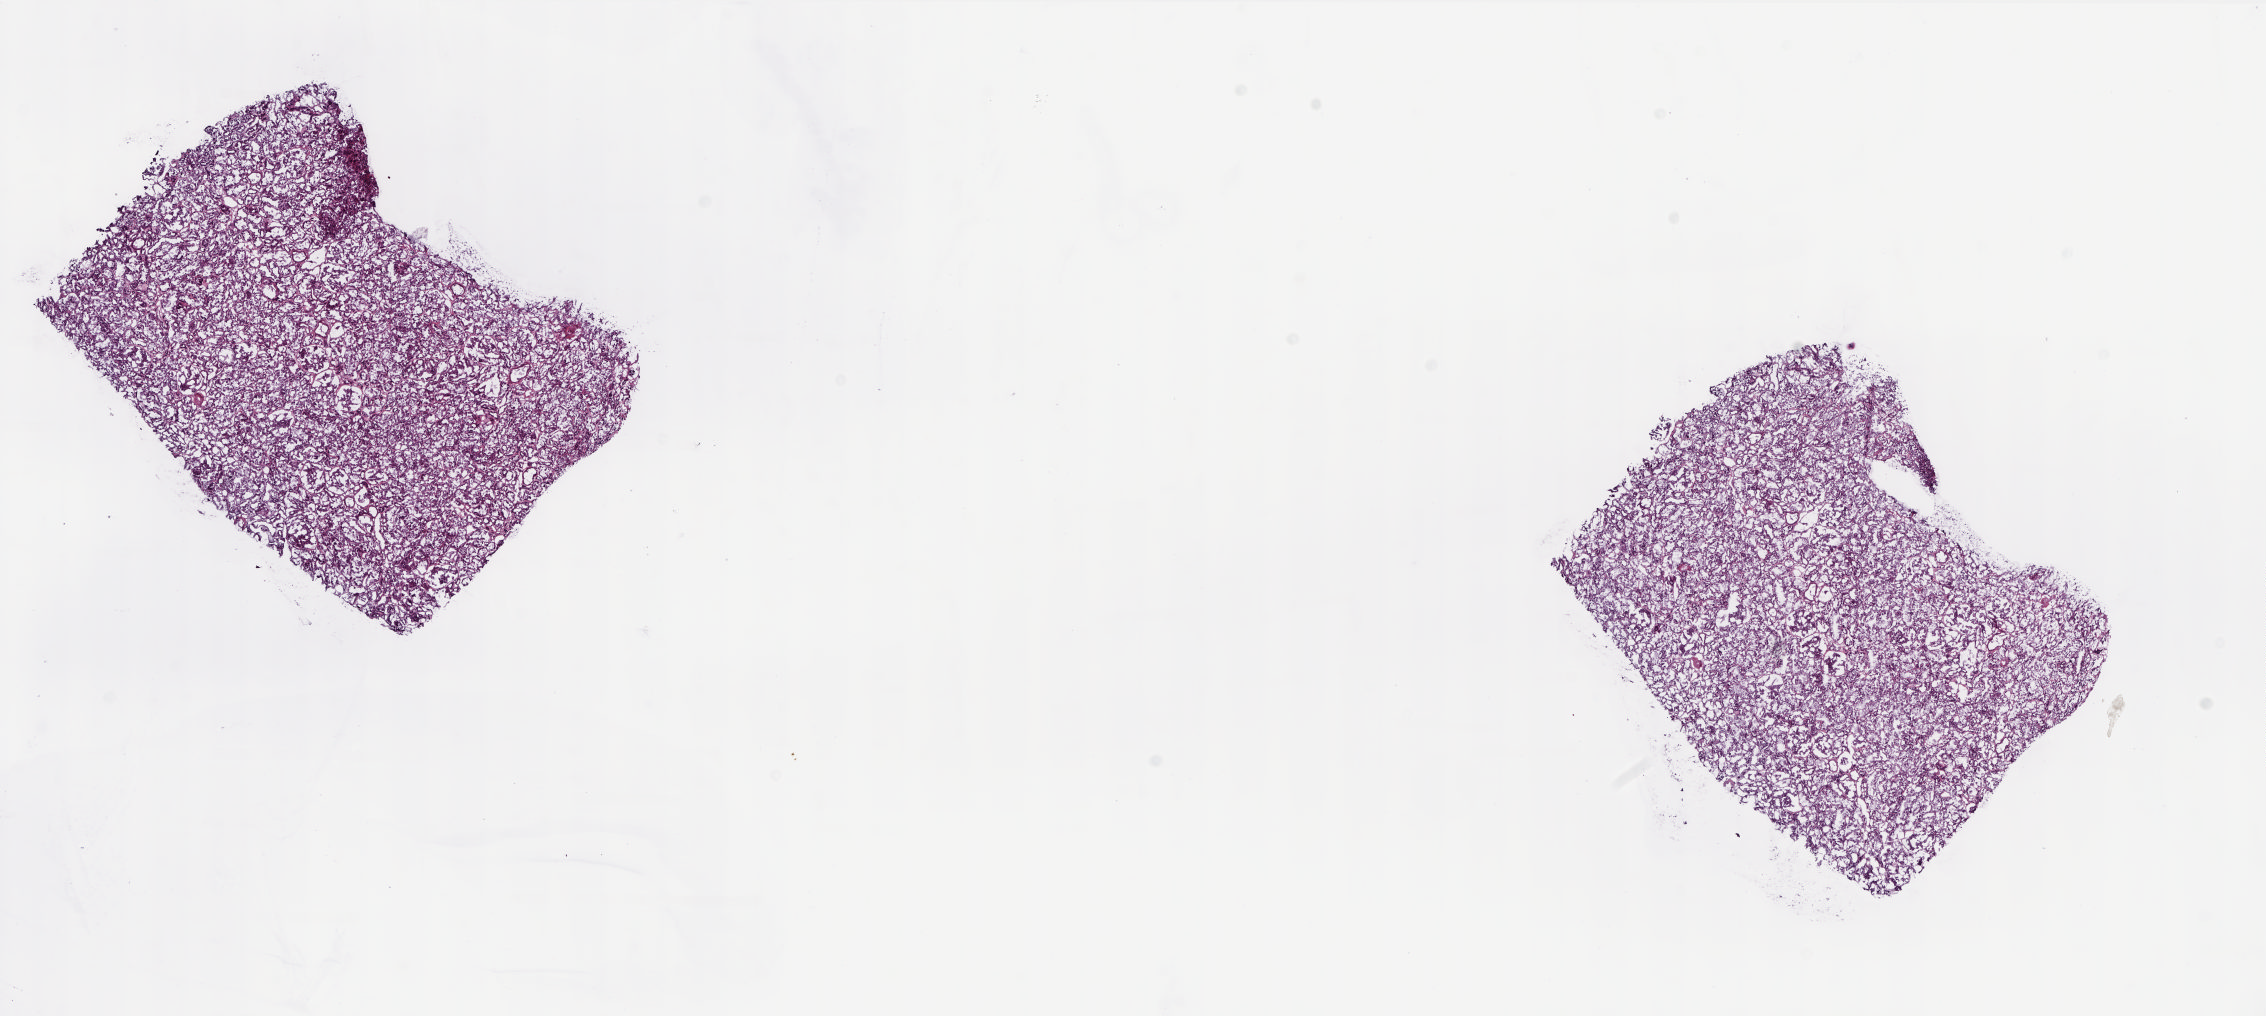
H&E whole-slide image — low-resolution overview of the scanned area, about 18.3 x 8.2 mm. Frozen section. Solid tissue normal (non-tumour tissue) sample from the adrenal cortex. Female, age 61 years at initial diagnosis. Composition of this section per pathologist review: tumour cells 0%, tumour nuclei 0%, normal cells 100%, stromal cells 0%, necrosis 0%. Inflammatory infiltration, as recorded: lymphocyte infiltration 0%, monocyte infiltration 0%, neutrophil infiltration 0%.
This section: solid tissue normal (non-tumour) sample from the same patient. Patient diagnosis: Adrenal cortical carcinoma (cortex of adrenal gland).